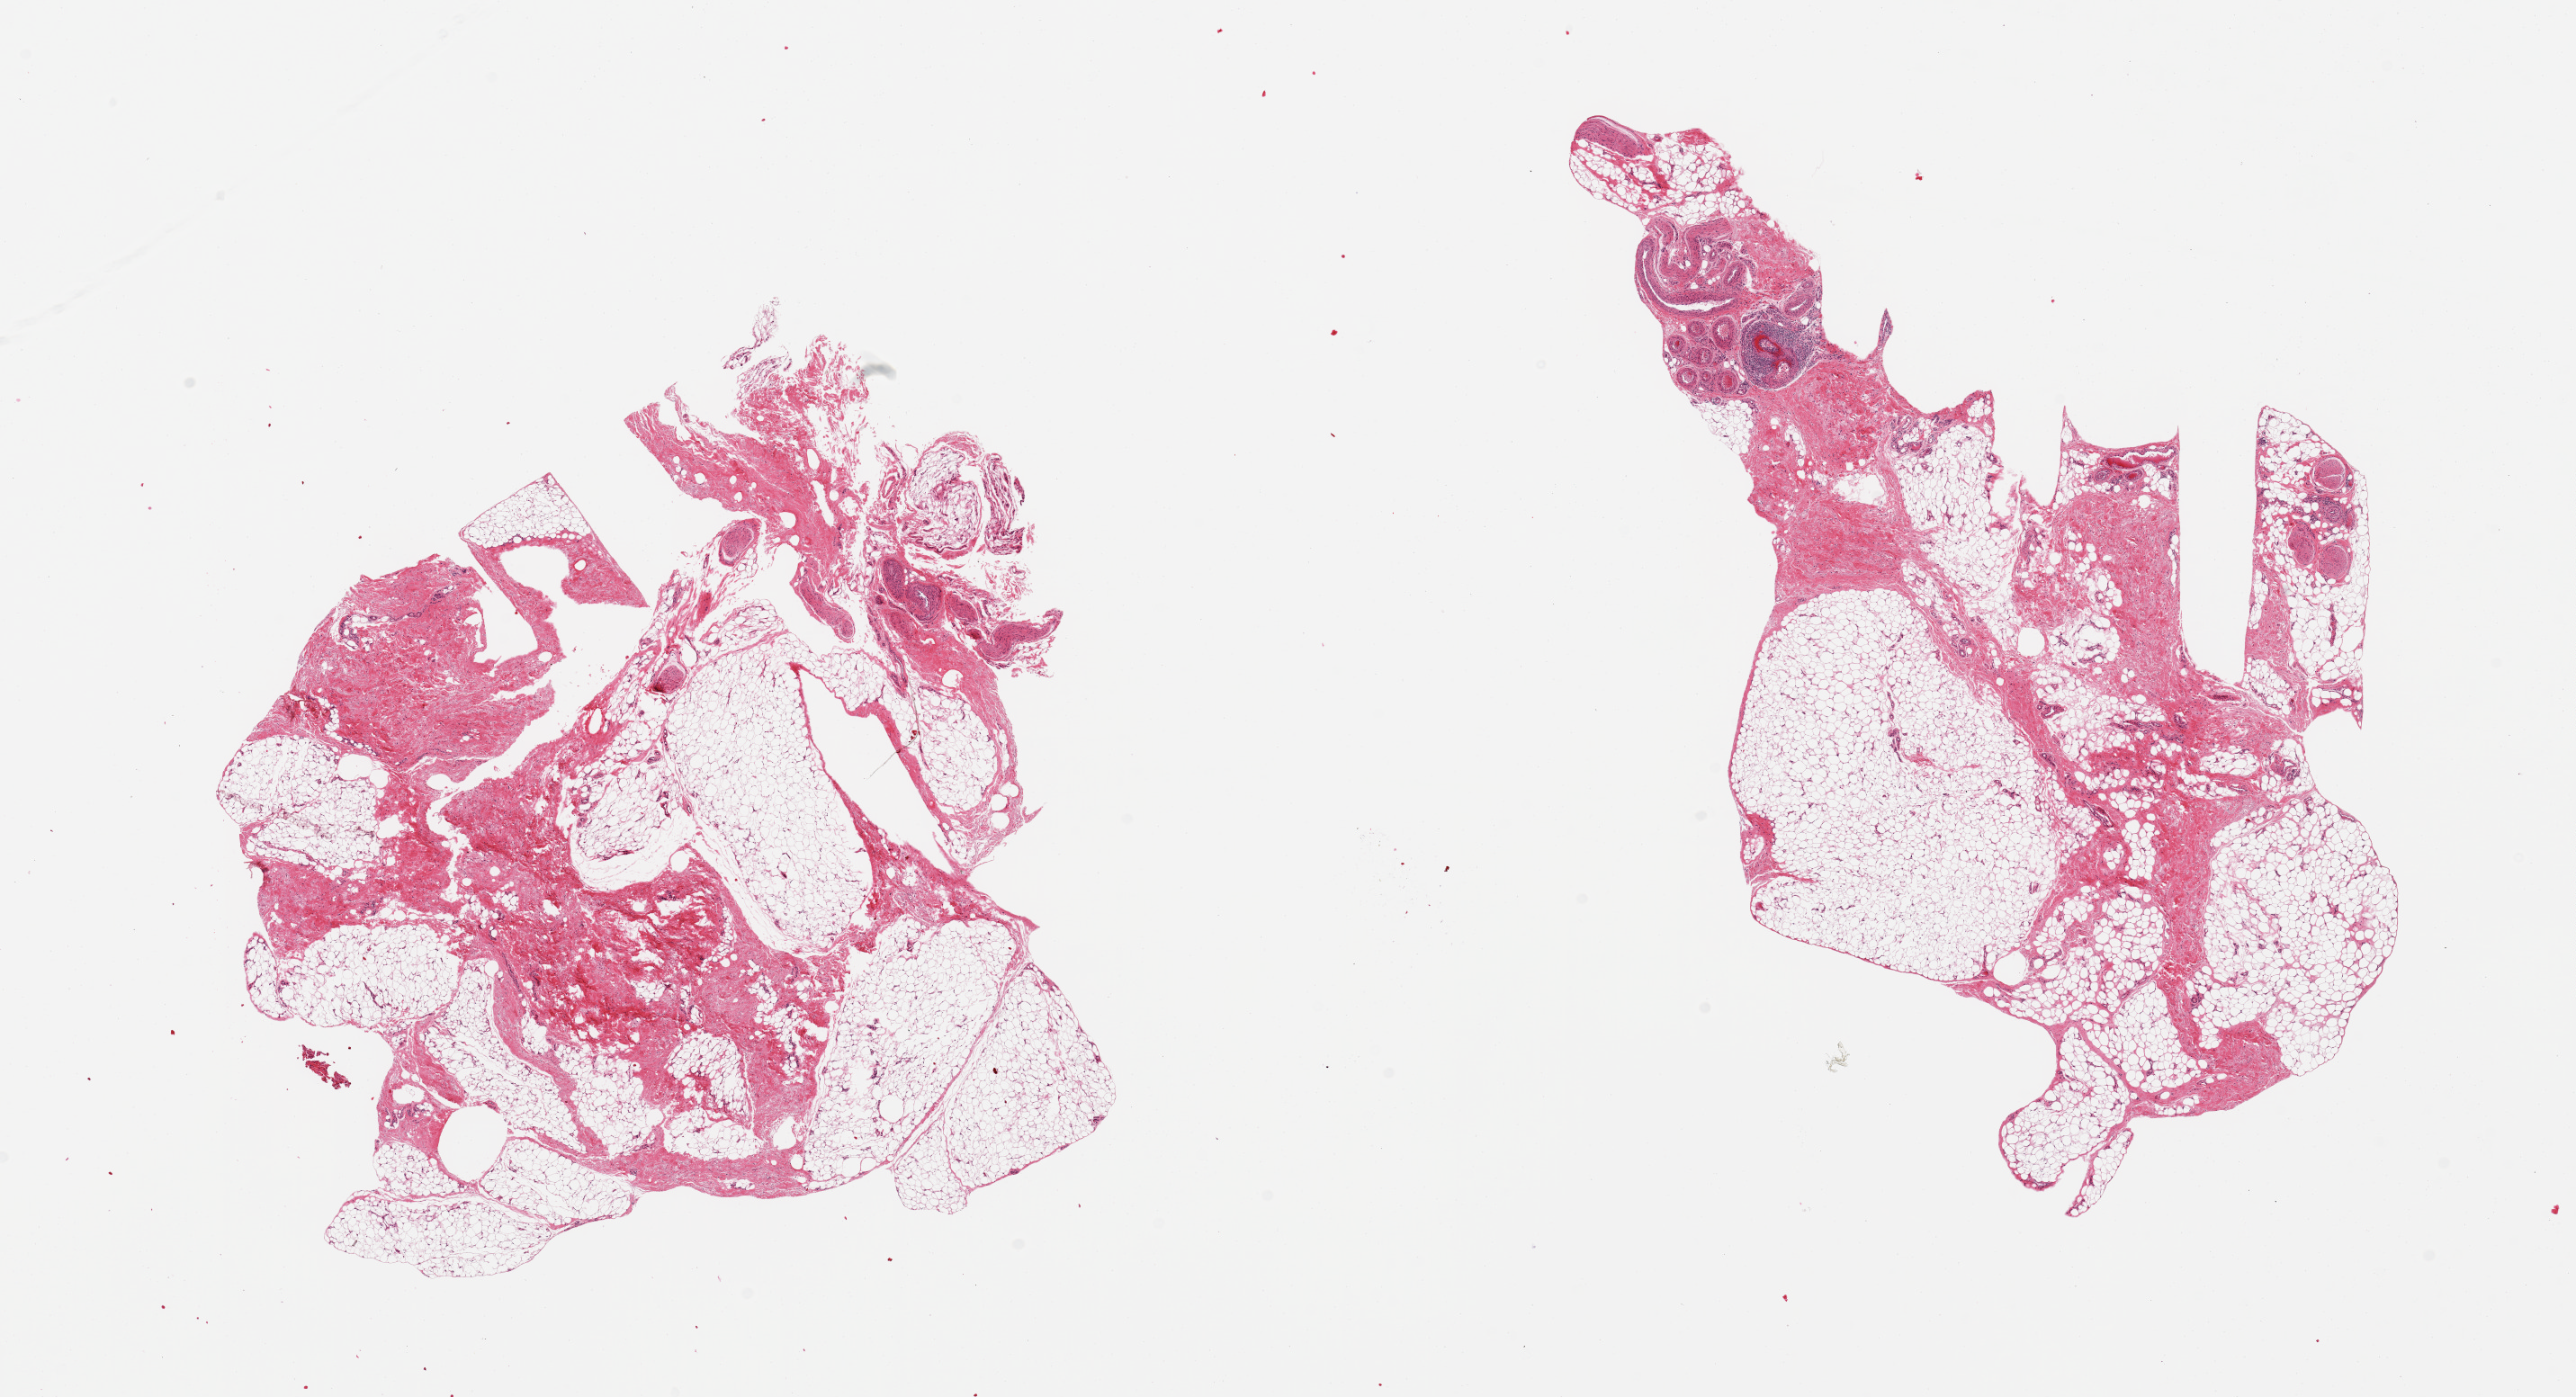
Whole-slide image, H&E stain, whole scanned area (about 22.6 x 12.3 mm) shown as a low-resolution overview, PAXgene-fixed, paraffin-embedded tissue, section of adipose tissue (target tissue), donor tissue sample. Donor: male.
Review note (as recorded): 2 pieces; 1 piece includes 30% fibrovascular tissue, 2nd includes 20% connective tissue, vessels, and nerves; focus of fibrinoid necrosis of vessel walls surrounded by lymphohistiocytic infiltrate.